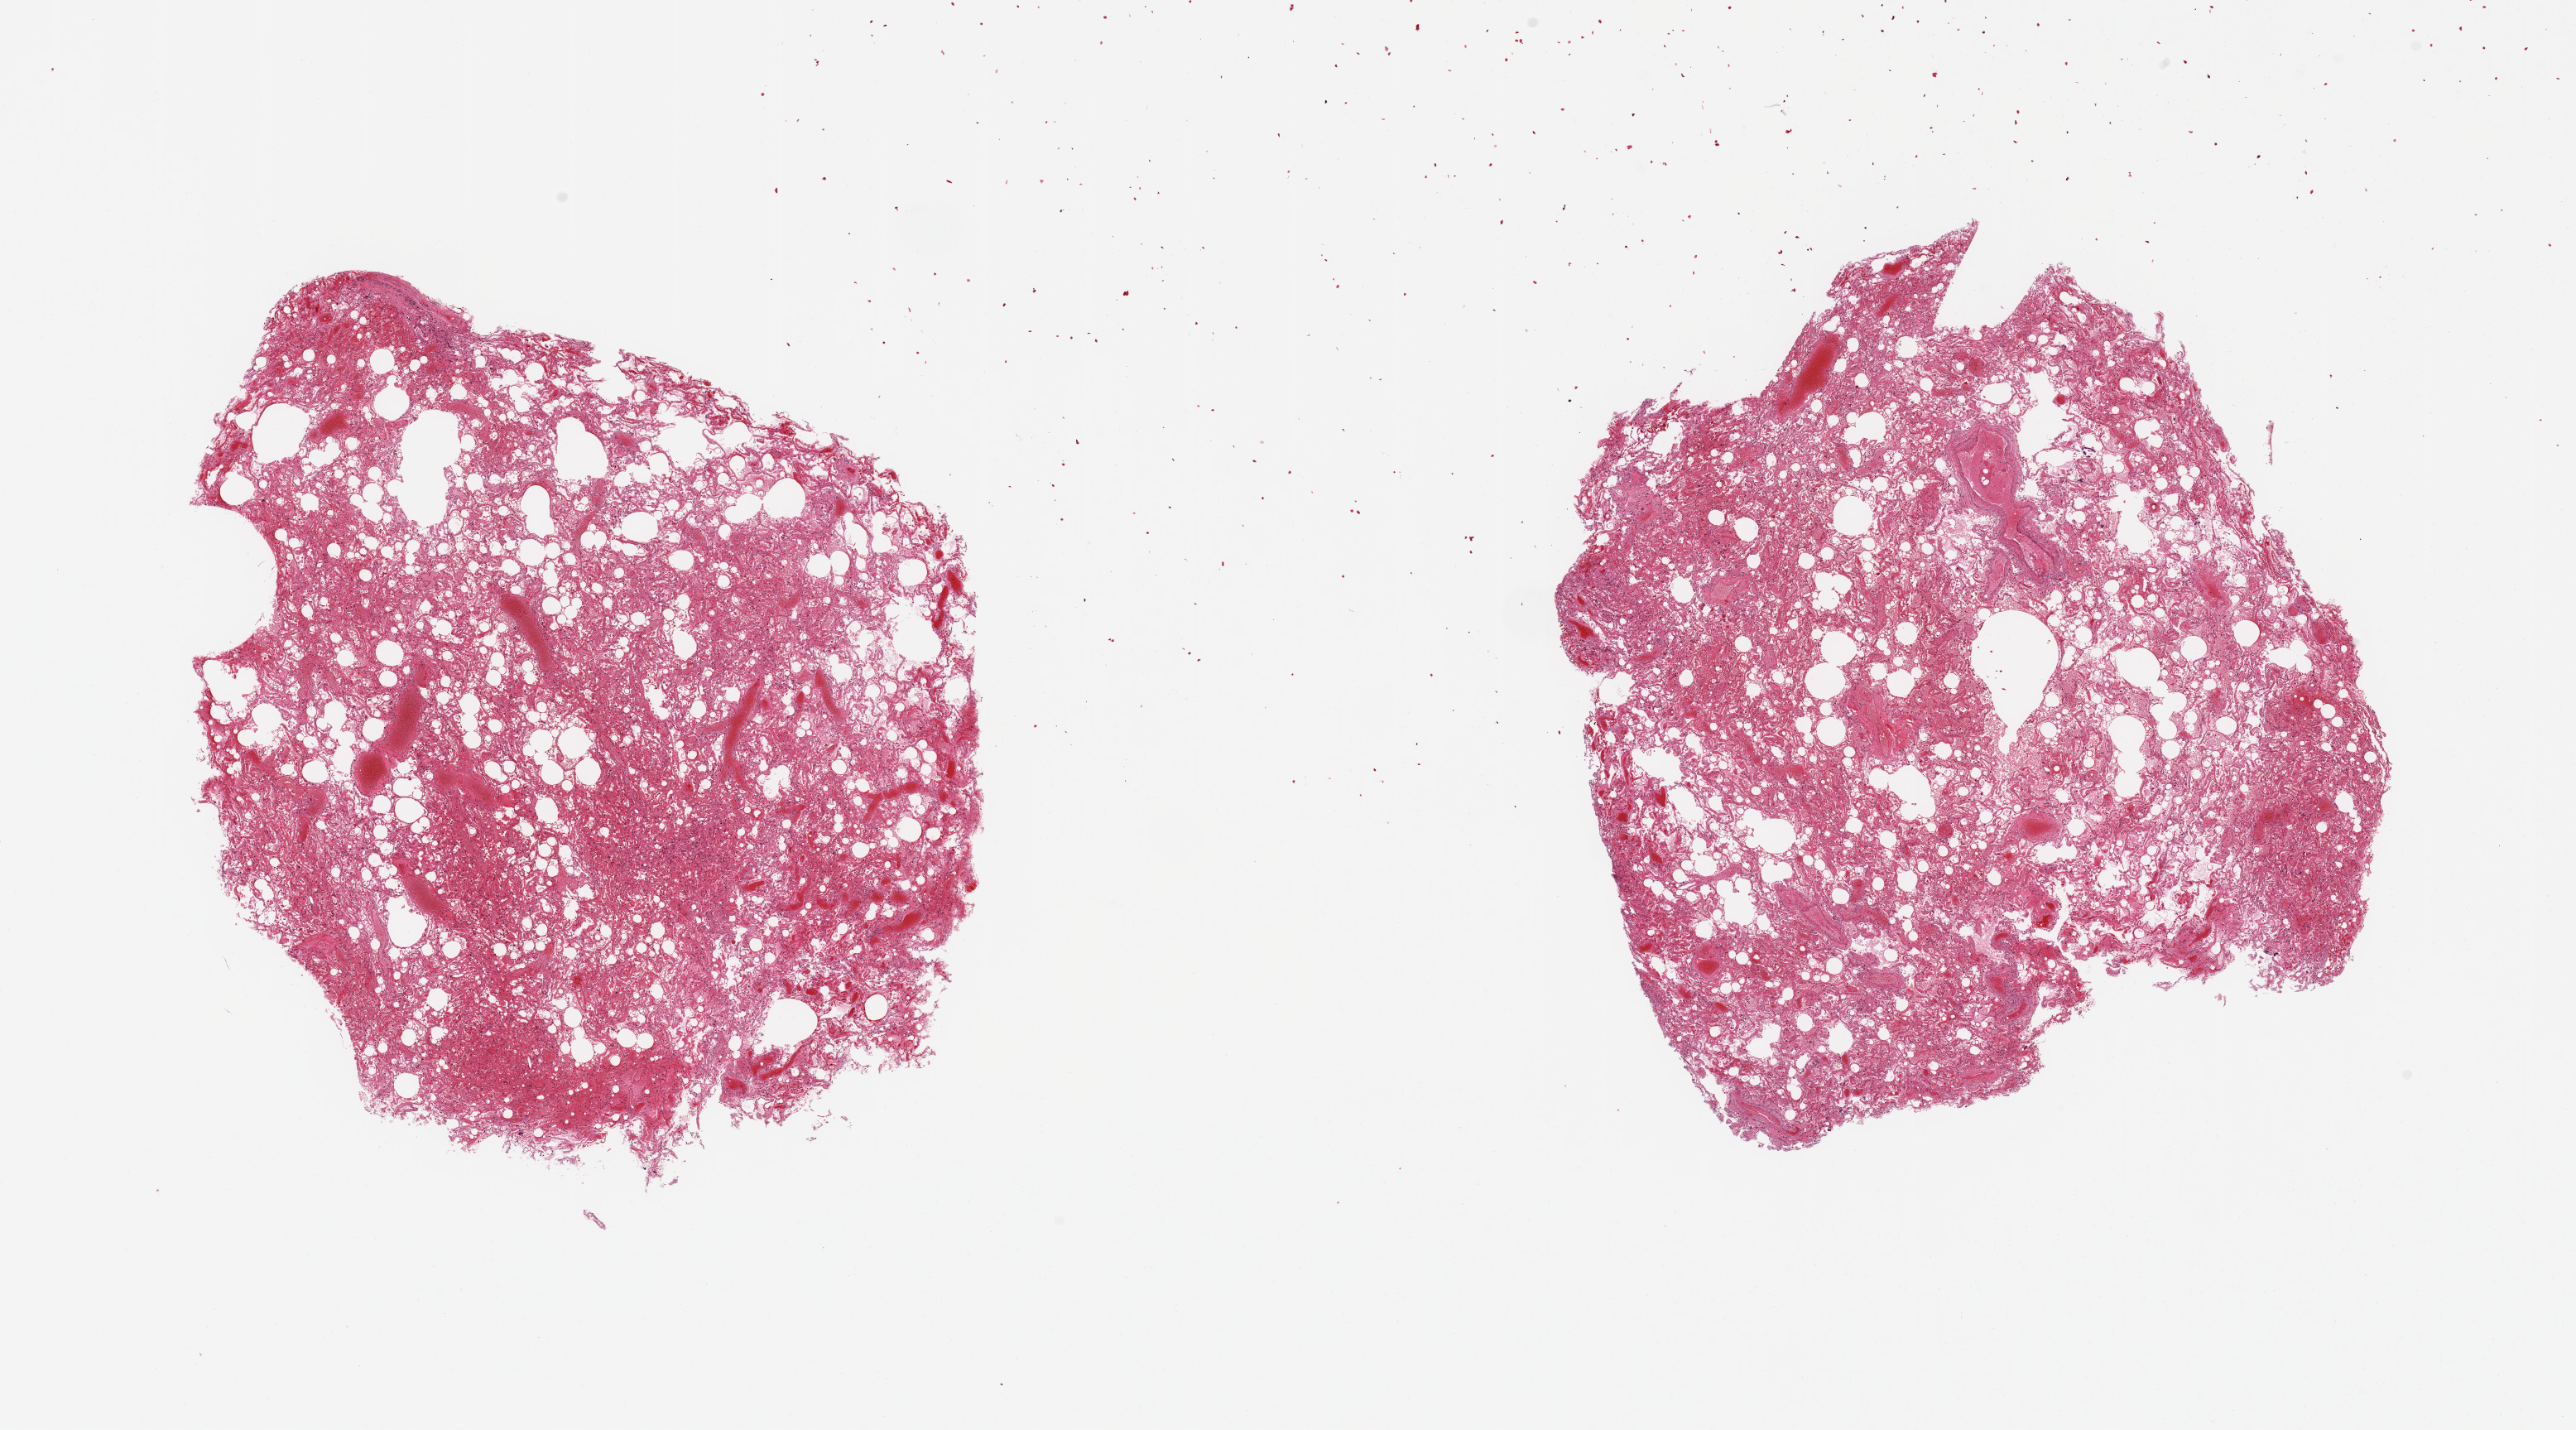
Haematoxylin and eosin whole-slide image, whole scanned area (about 24.6 x 13.7 mm) shown as a low-resolution overview; PAXgene-fixed paraffin-embedded (PFPE) section; target tissue: lung; donor tissue sample.
Pathologist's review note for this sample: 2 pieces, moderate edema, congestion.